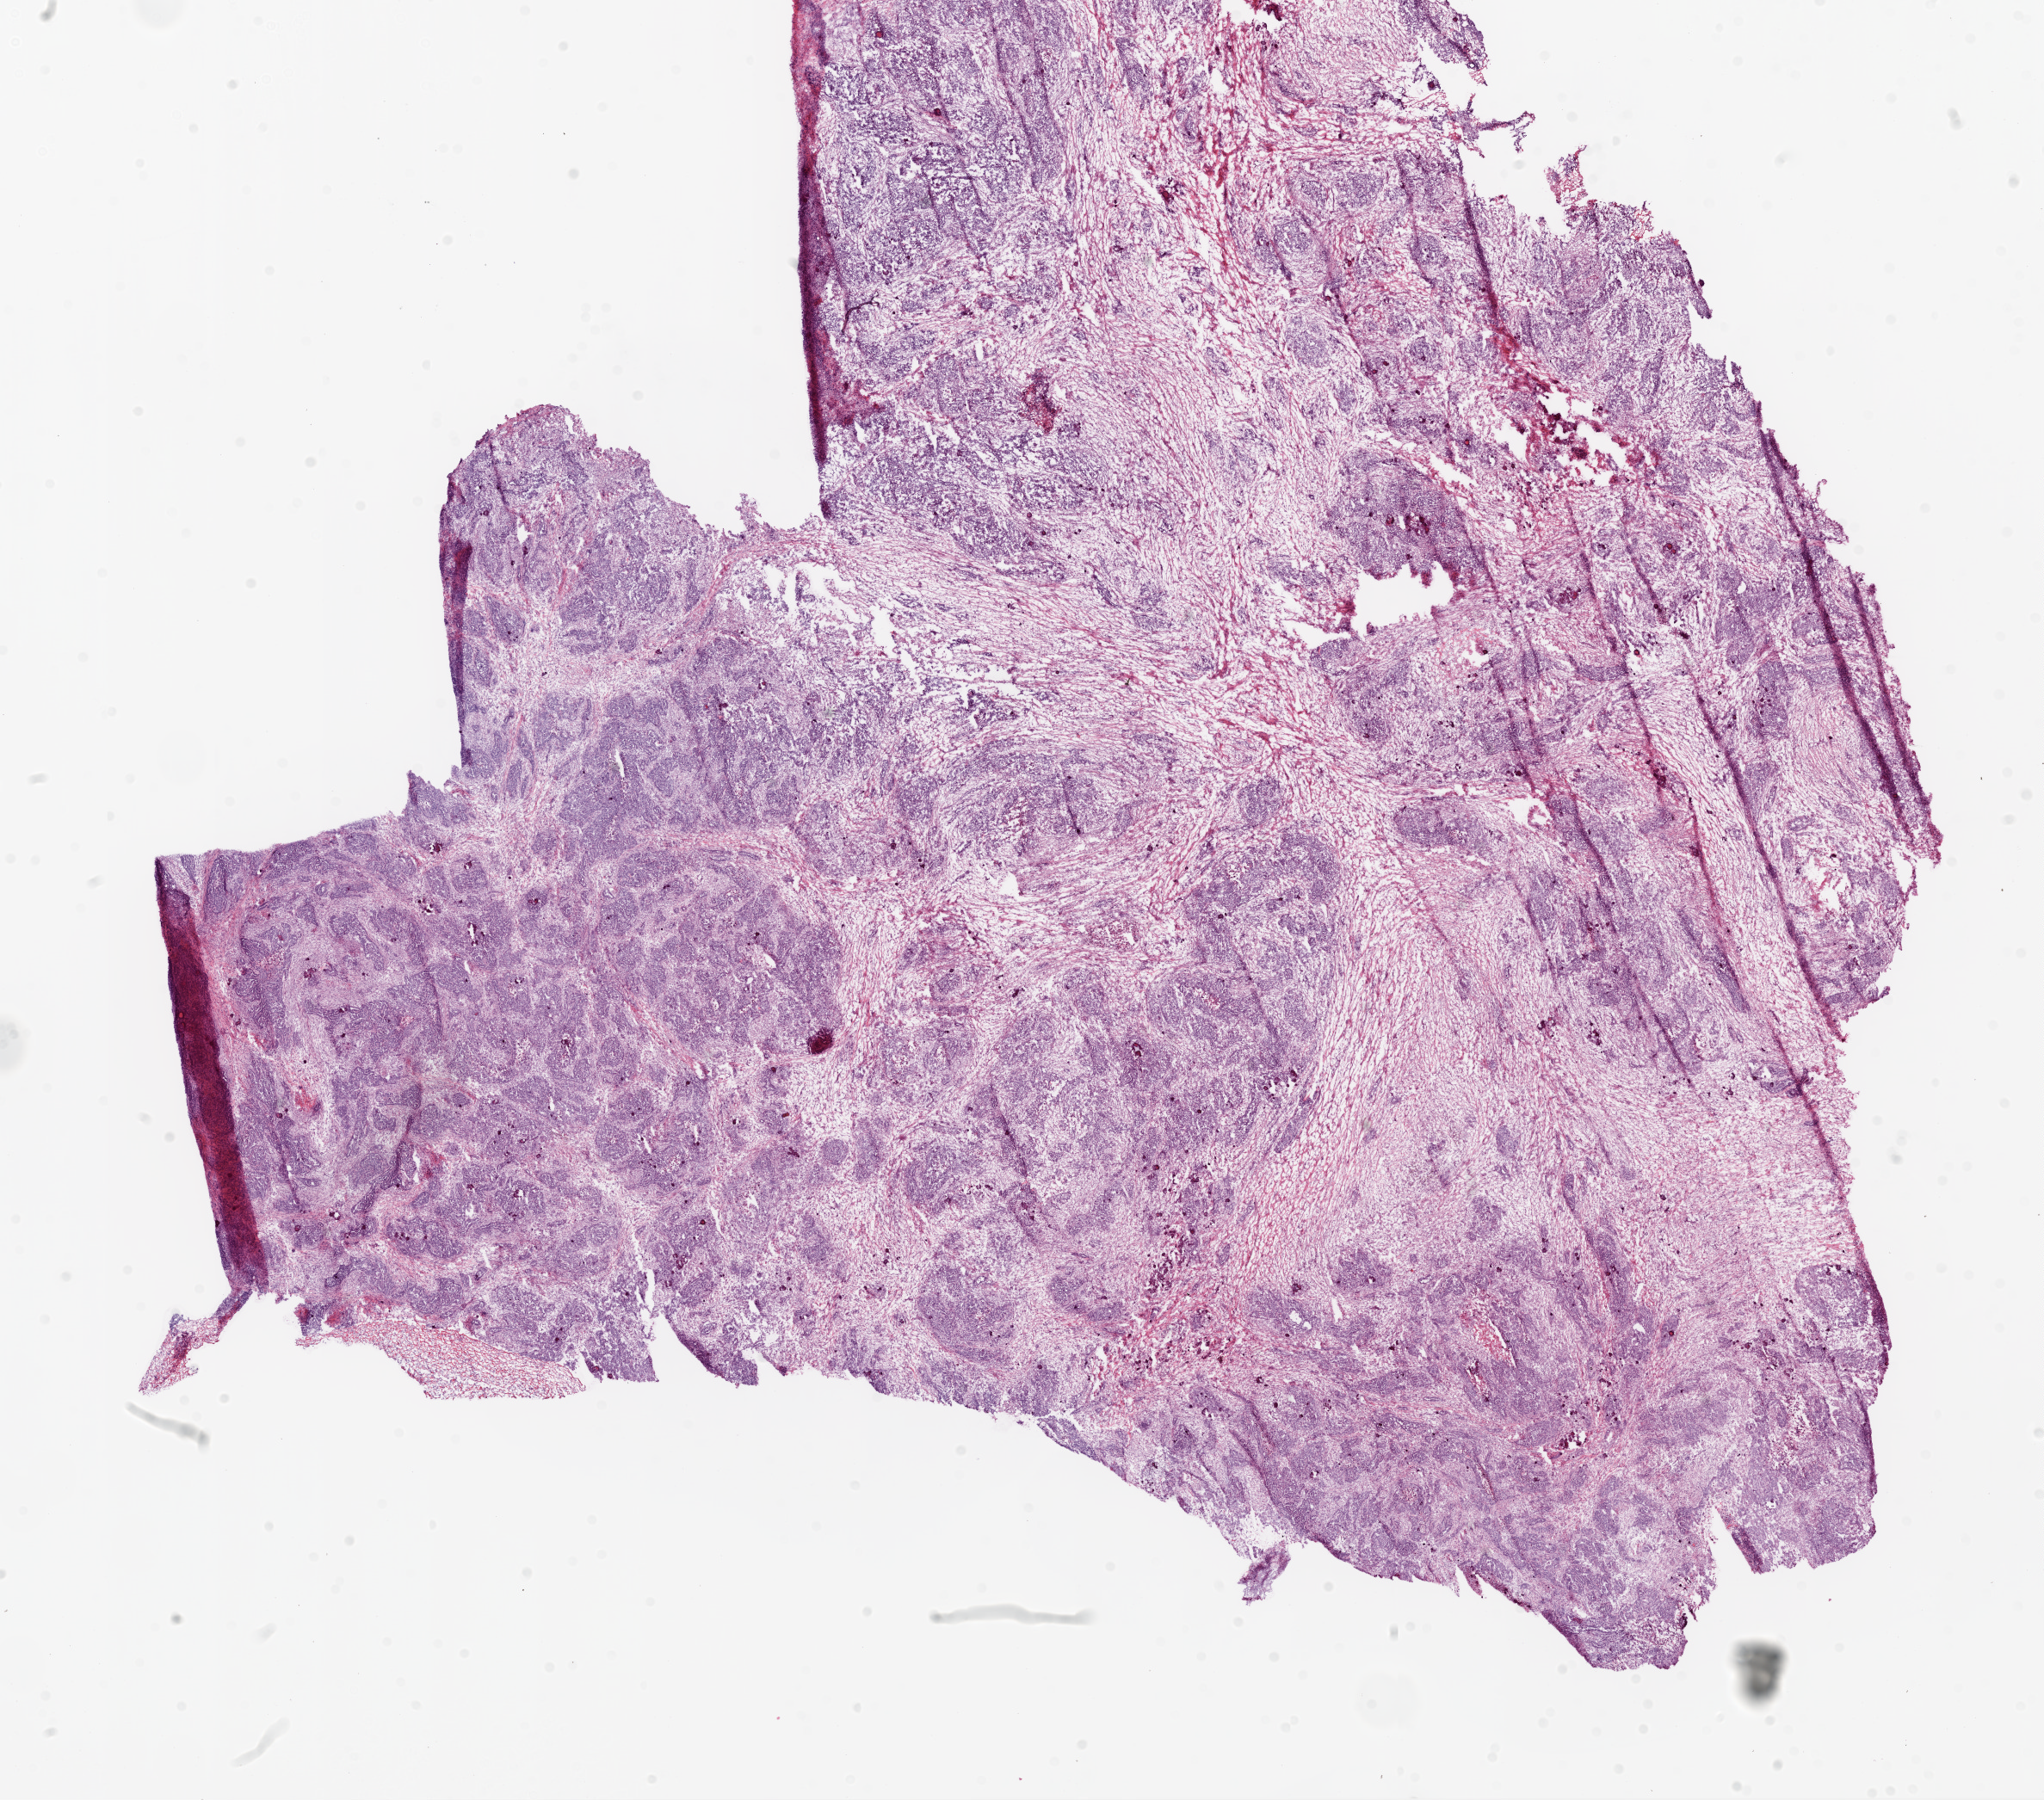
Whole-slide histology image, Hematoxylin and eosin (H&E) stained — a low-resolution overview of the entire scanned area, about 19.1 x 16.8 mm (slide scanned at 20x); frozen section from the bottom of the tissue portion; primary tumour sample from the ovary. Female patient; age at initial diagnosis 71 years. Histologic grade: G3 (poorly differentiated). Slide review estimates, as recorded: tumour cells 70%, tumour nuclei 75%, normal cells 0%, stromal cells 25%, necrosis 5%.
FIGO stage: IIIC. Histologic diagnosis: Serous cystadenocarcinoma, NOS.